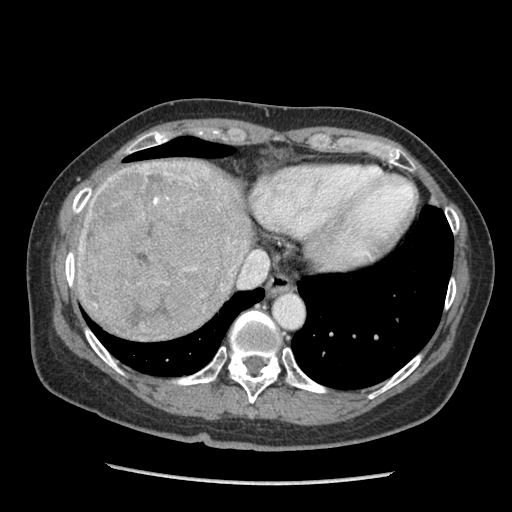
Contrast-enhanced abdominal CT (liver protocol), one axial slice; position 80 of 105 along the scan axis; 140 kVp; soft-tissue window (W 400 / L 40 HU); 2.5 mm slice thickness; 512 × 512 image matrix, field of view 340 × 340 mm. Case-level facts recorded for this patient, not image findings: diagnosis: hepatocellular carcinoma (patient treated with transarterial chemoembolisation; whether this scan precedes or follows treatment is not stated here); TNM stage (as recorded): Stage-I; Child-Pugh class: A; tumour differentiation: moderately differentiated; tumour nodularity: uninodular.
Structures marked on this image (semi-automatically segmented with operator editing):
- liver parenchyma outside the tumour (the mass and vessels are separate outlines, so this box may not span the whole liver): bounding box [x1, y1, x2, y2] px = [74, 160, 252, 332]
- mass: [78, 161, 233, 340]